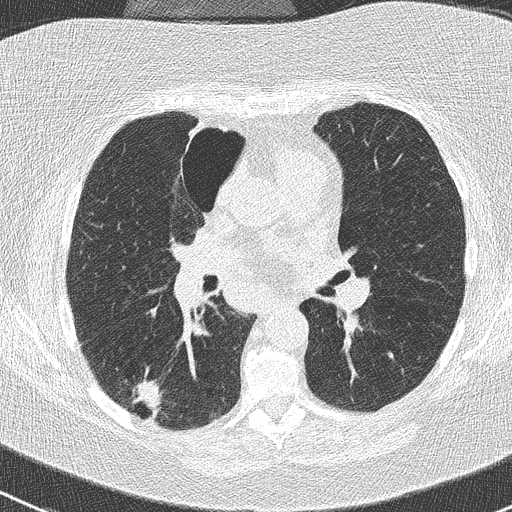
Low-dose screening chest CT, axial slice. First (baseline) screen. Lung window (W 1500 / L -600 HU). 2 mm slice thickness. 120 kVp. Slice 119 of 261 in the series. 512 × 512 image matrix. Female participant, aged 74 years at enrolment.
• Expert-annotated lung lesion, bounding box [x1, y1, x2, y2] px = [120, 374, 175, 429].
• The screening reader recorded 3 non-calcified nodules or masses ≥4 mm on this exam; which of them this box marks is not recorded.
• Official screen result: positive, change unspecified: nodule(s) >= 4 mm or enlarging nodule(s), mass(es), or other non-specific abnormalities suspicious for lung cancer.